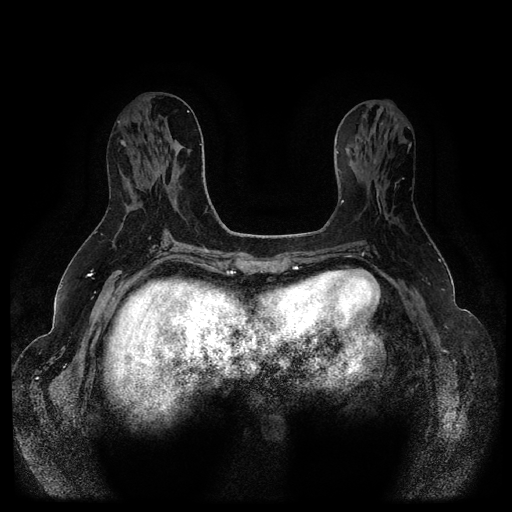
Breast MRI (dynamic contrast-enhanced, multi-phase), one axial slice; slice 44 of 116 in the series (ordered by position); dynamic contrast-enhanced series, time point 2 of 5 at this slice position (early post-contrast); 1.5 T; TE 2.6 ms, TR 5.3 ms; 2 mm slice thickness; 512 × 512 image matrix, field of view 350 × 350 mm. Patient: female, 54 years.
Annotated regions visible in this slice (semi-automatically segmented with operator editing):
- breast lesion (labelled benign in the annotation): bounding box [x1, y1, x2, y2] px = [120, 140, 126, 147]